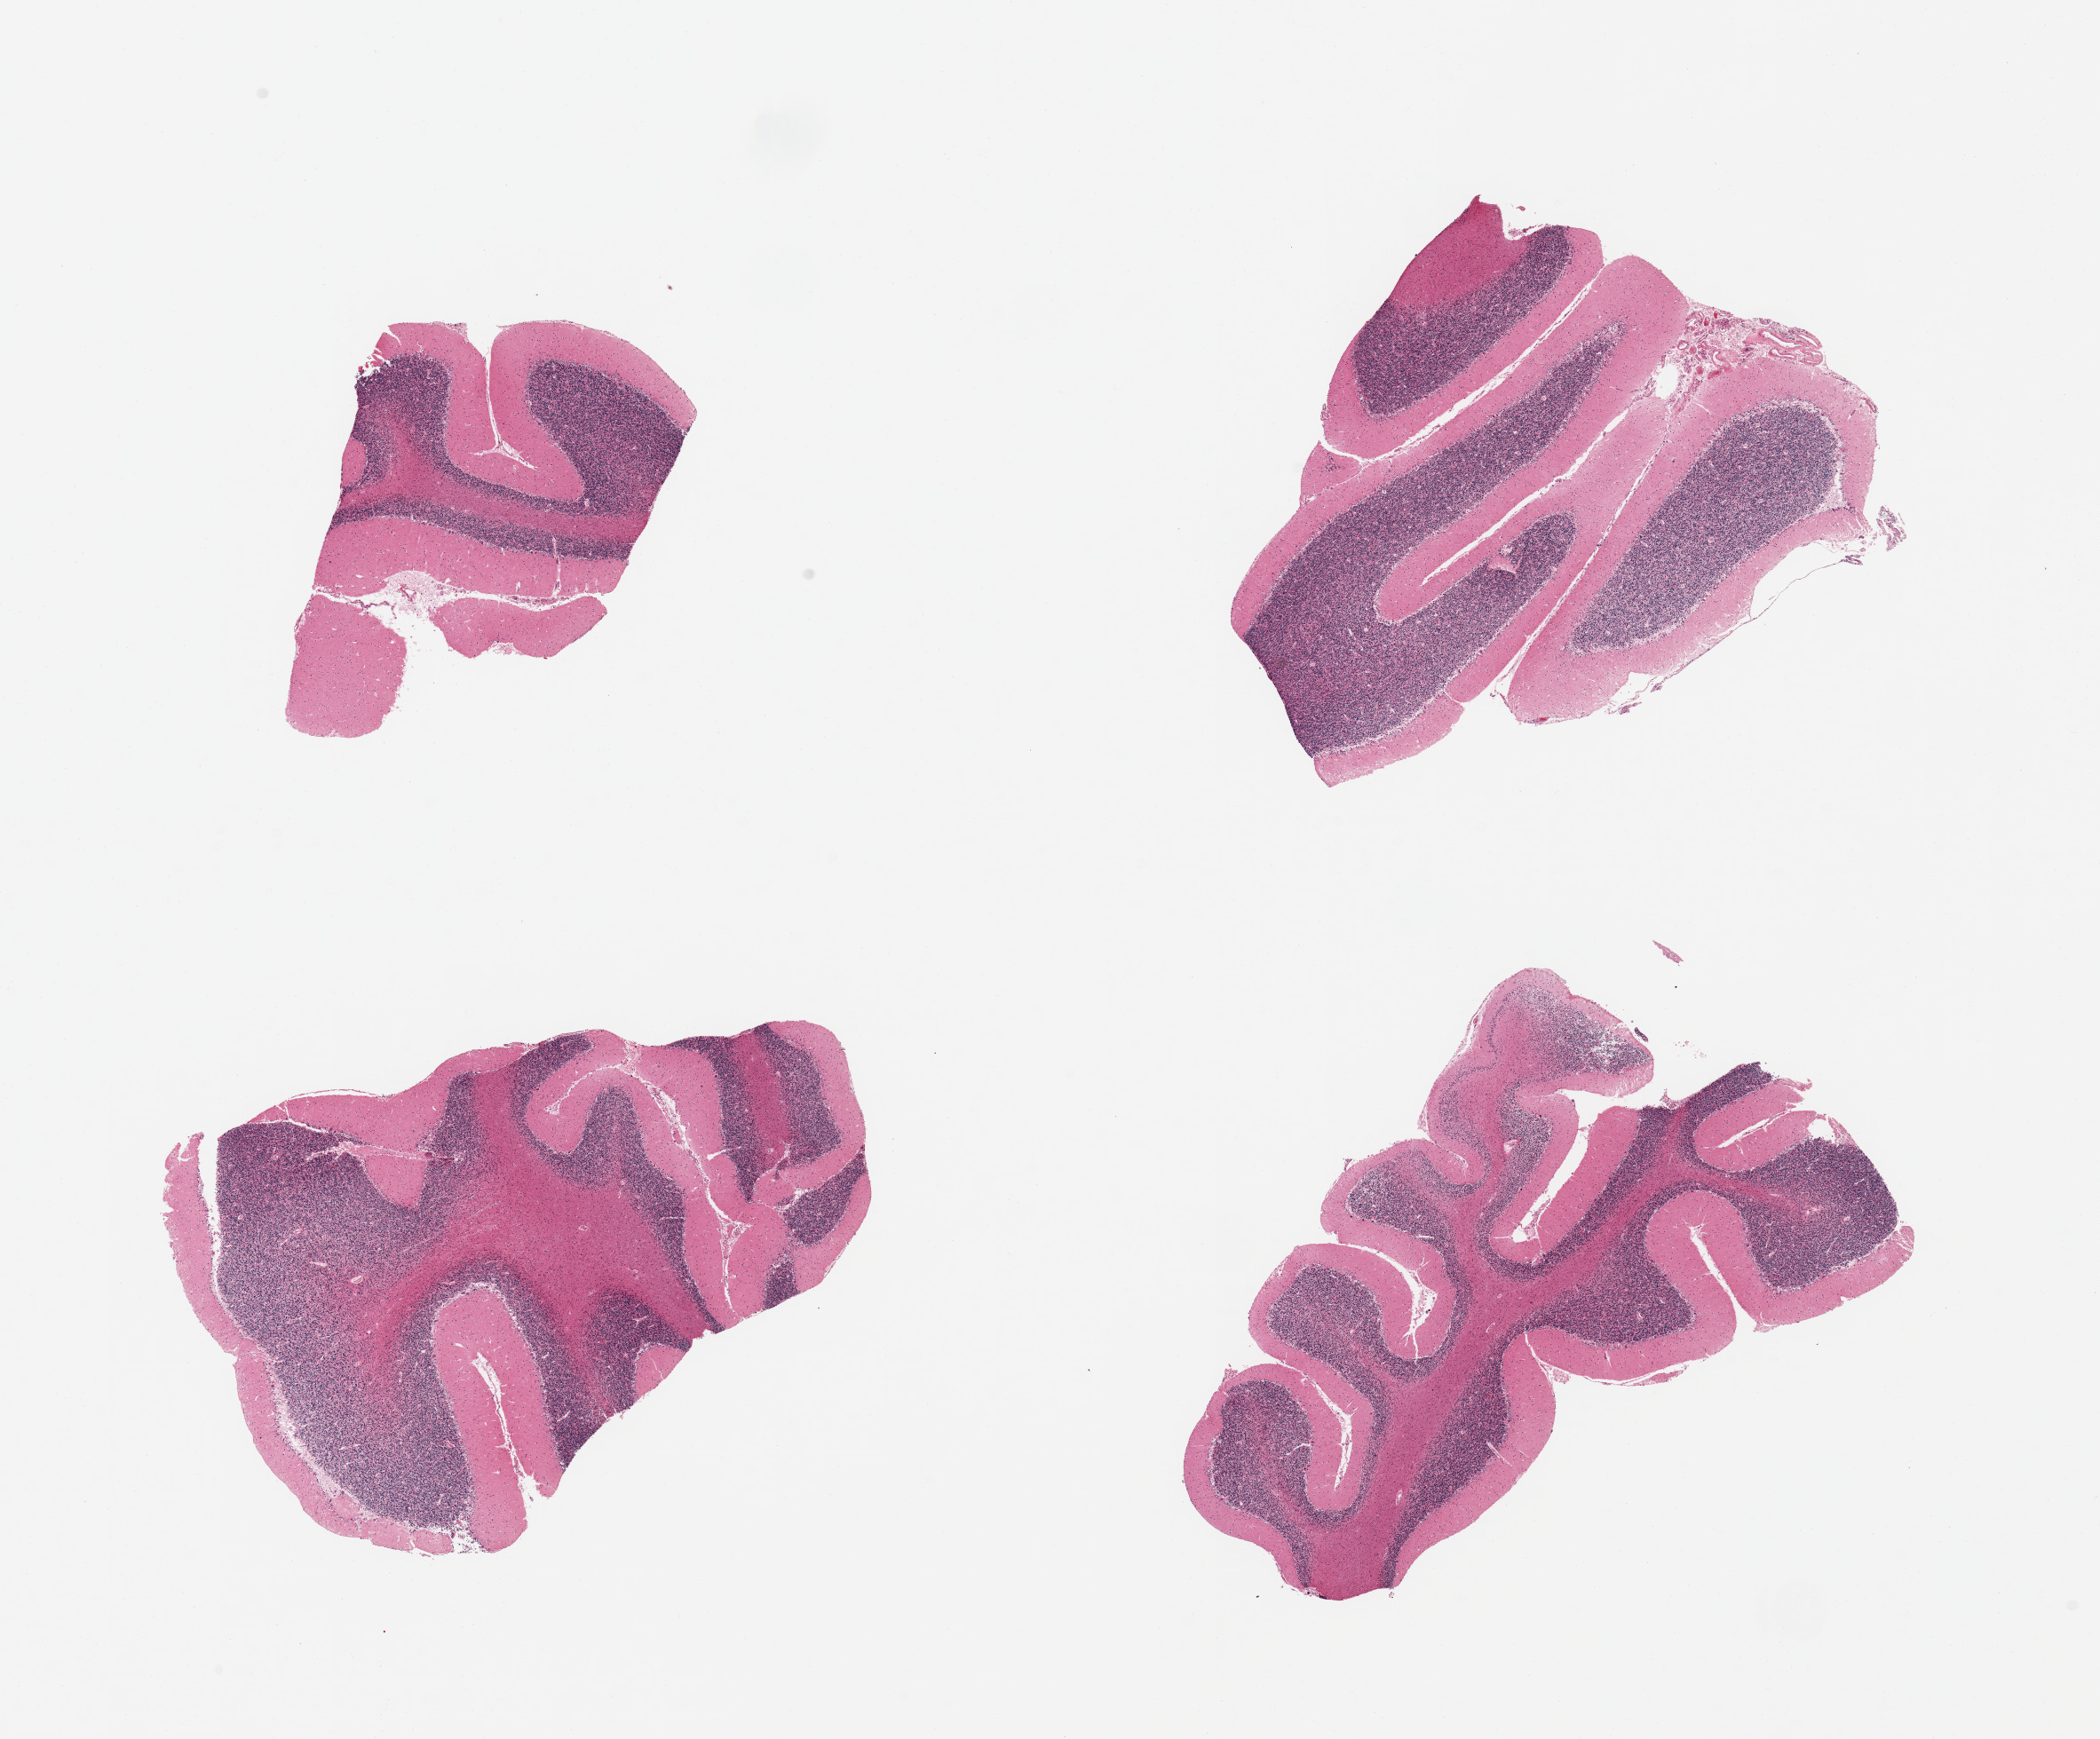
Hematoxylin and eosin (H&E) whole-slide image, brightfield, low-resolution overview of the scanned area, about 18.7 x 15.5 mm (from a 20x scan). PAXgene-fixed, paraffin-embedded tissue. Sampled site (target tissue): cerebellum. Tissue donor sample. Donor: male.
Pathologist's review note for this sample: 4 pieces, no abnormalities.